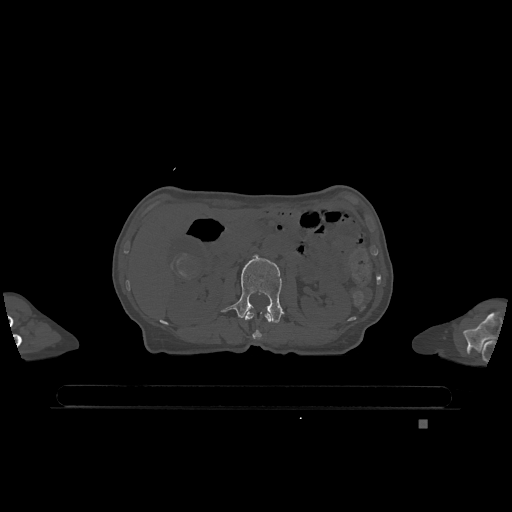
CT including the spine, one axial slice; slice 429 of 1317 in the series (ordered by position); bone window (W 1800 / L 400 HU); 0.5 mm slice thickness; 512 × 512 image matrix, field of view 500 × 500 mm. Patient: female, 74 years. From the clinical record (not read from this slice): primary cancer: lung; vertebrae with lytic lesions (as recorded): T1, T4, T5, T6, L4, L5.
Structures marked on this image (semi-automatic segmentation, software-assisted and operator-edited):
- L1 vertebra: box from (x=243, y=311) to (x=272, y=339) px
- L2 vertebra: (x=222, y=255)–(x=283, y=323)